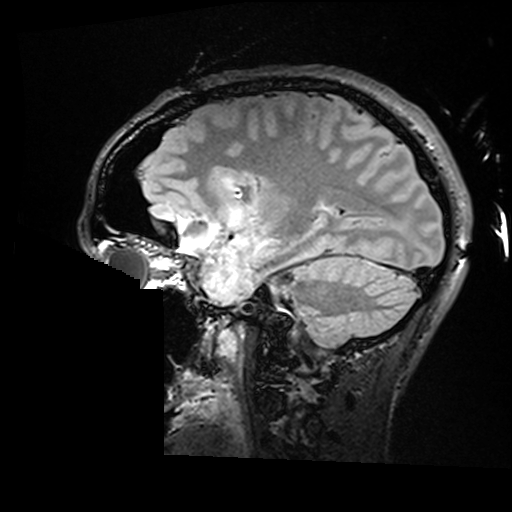
Brain MRI from a brain-tumour surgery series, one sagittal slice. Slice 108 of 176 in the series (ordered by position). T2 FLAIR. 1 mm slice thickness. 512 × 512 image matrix, field of view 250 × 250 mm. Case-level facts recorded for this patient, not image findings: histopathology: Astrocytoma; WHO grade: 2; IDH mutation: yes.
Structures marked on this image (outlined manually by an expert reader):
- residual tumour: box from (x=224, y=179) to (x=272, y=190) px